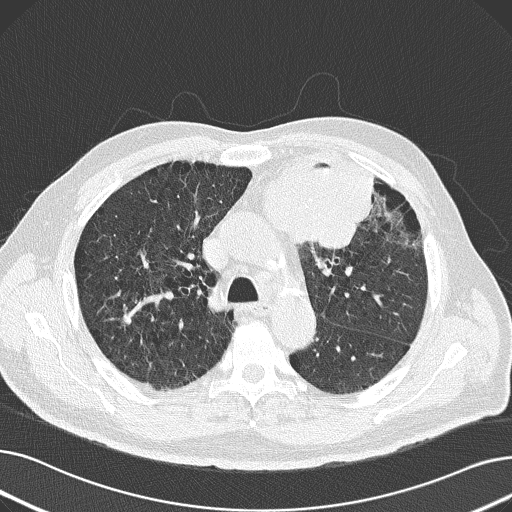
Axial slice from a low-dose chest CT screening exam, baseline screening round, lung window (W 1500 / L -600 HU), slice 60 of 165 in the series, 512 × 512 image matrix. Male, age 69 years at enrolment. Former smoker at enrolment.
• Expert reader's lesion annotation, bounding box [x1, y1, x2, y2] px = [228, 144, 380, 253].
• Reader record for this screening exam (exam-level; its link to the box is not recorded): non-calcified nodule or mass ≥4 mm, left upper lobe, 6 × 10 mm, spiculated (stellate) margins, soft tissue attenuation.
• Official screen result: positive, change unspecified: nodule(s) >= 4 mm or enlarging nodule(s), mass(es), or other non-specific abnormalities suspicious for lung cancer.
• Later outcome: lung cancer diagnosed 20 days after this screen — non-small cell carcinoma, left upper lobe, poorly differentiated (G3), stage IB (AJCC 6th edition), 100 mm at pathology.